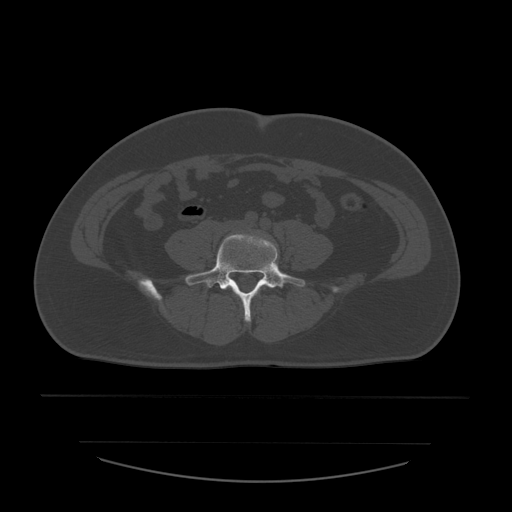
CT including the spine, one axial slice. Position 126 of 532 along the scan axis. Reconstruction kernel STANDARD. 120 kVp. Bone window (W 1800 / L 400 HU). 512 × 512 image matrix, field of view 441 × 441 mm. Patient age 44 years. From the clinical record (not read from this slice): primary cancer: soft tissue sarcoma.
Annotated regions visible in this slice (semi-automatic segmentation, software-assisted and operator-edited):
- L5 vertebra: bounding box (x1, y1, x2, y2) in pixels: (184, 234, 305, 322)